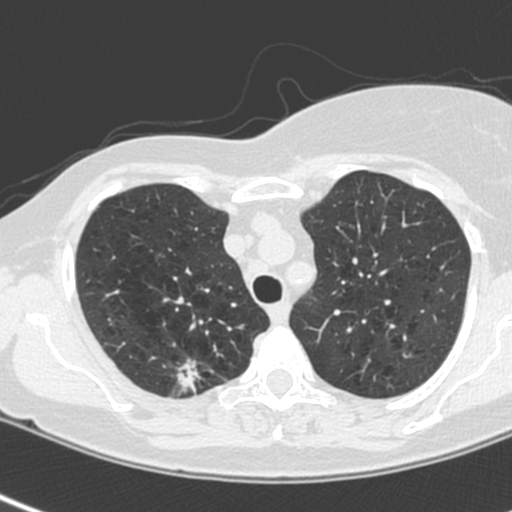
Axial slice from a low-dose chest CT screening exam. Baseline screening round. Lung window (W 1500 / L -600 HU). 1.3 mm slice thickness. Slice 41 of 214 in the series. 512 × 512 image matrix. Female, age 64 years at enrolment.
Expert reader's lesion annotation, bounding box <165,355,220,405> (left, top, right, bottom; pixels). Screening reader's record for this exam (one nodule recorded; not confirmed to be the boxed lesion): non-calcified nodule or mass ≥4 mm, right upper lobe, 13 × 10 mm, spiculated (stellate) margins, soft tissue attenuation. Lung cancer was diagnosed 21 days after this screen: adenocarcinoma, NOS, right upper lobe, poorly differentiated (G3), stage IIIB (AJCC 6th edition), 20 mm at pathology.